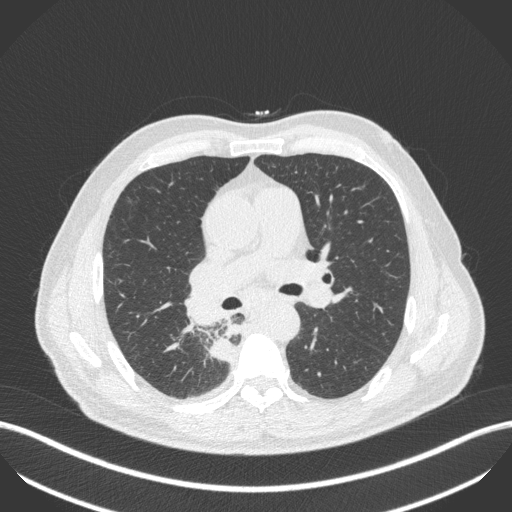
Chest CT, one axial slice; position 273 of 451 along the scan axis; 100 kVp; lung window (W 1500 / L -600 HU); 512 × 512 image matrix. Male patient, age 61 years. From the clinical record (not read from this slice): clinical TNM (as recorded): T1 N0 M0; histopathological grade: G3.
Structures marked on this image (rectangle marked by the reading radiologist):
- lung tumour (recorded histology: small cell carcinoma): box from (x=207, y=336) to (x=239, y=369) px